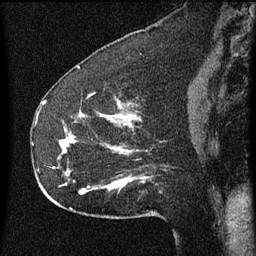
Breast MRI (dynamic contrast-enhanced), one sagittal slice; position 23 of 60 along the scan axis; dynamic contrast-enhanced series, image 2 of 3 at this slice position (ordered by acquisition); 1.5 T; TE 4.2 ms, TR 8 ms; 256 × 256 image matrix, field of view 180 × 180 mm. Female patient, age 52 years.
Structures marked on this image (semi-automatic segmentation, software-assisted and operator-edited):
- analysis volume of interest (the breast-tissue region the enhancement analysis was run in; not a lesion): bounding box <54,110,149,207> (left, top, right, bottom; pixels)
- tumour enhancement mask (voxels above the 70 % enhancement threshold inside the analysis volume of interest): <60,116,132,193>